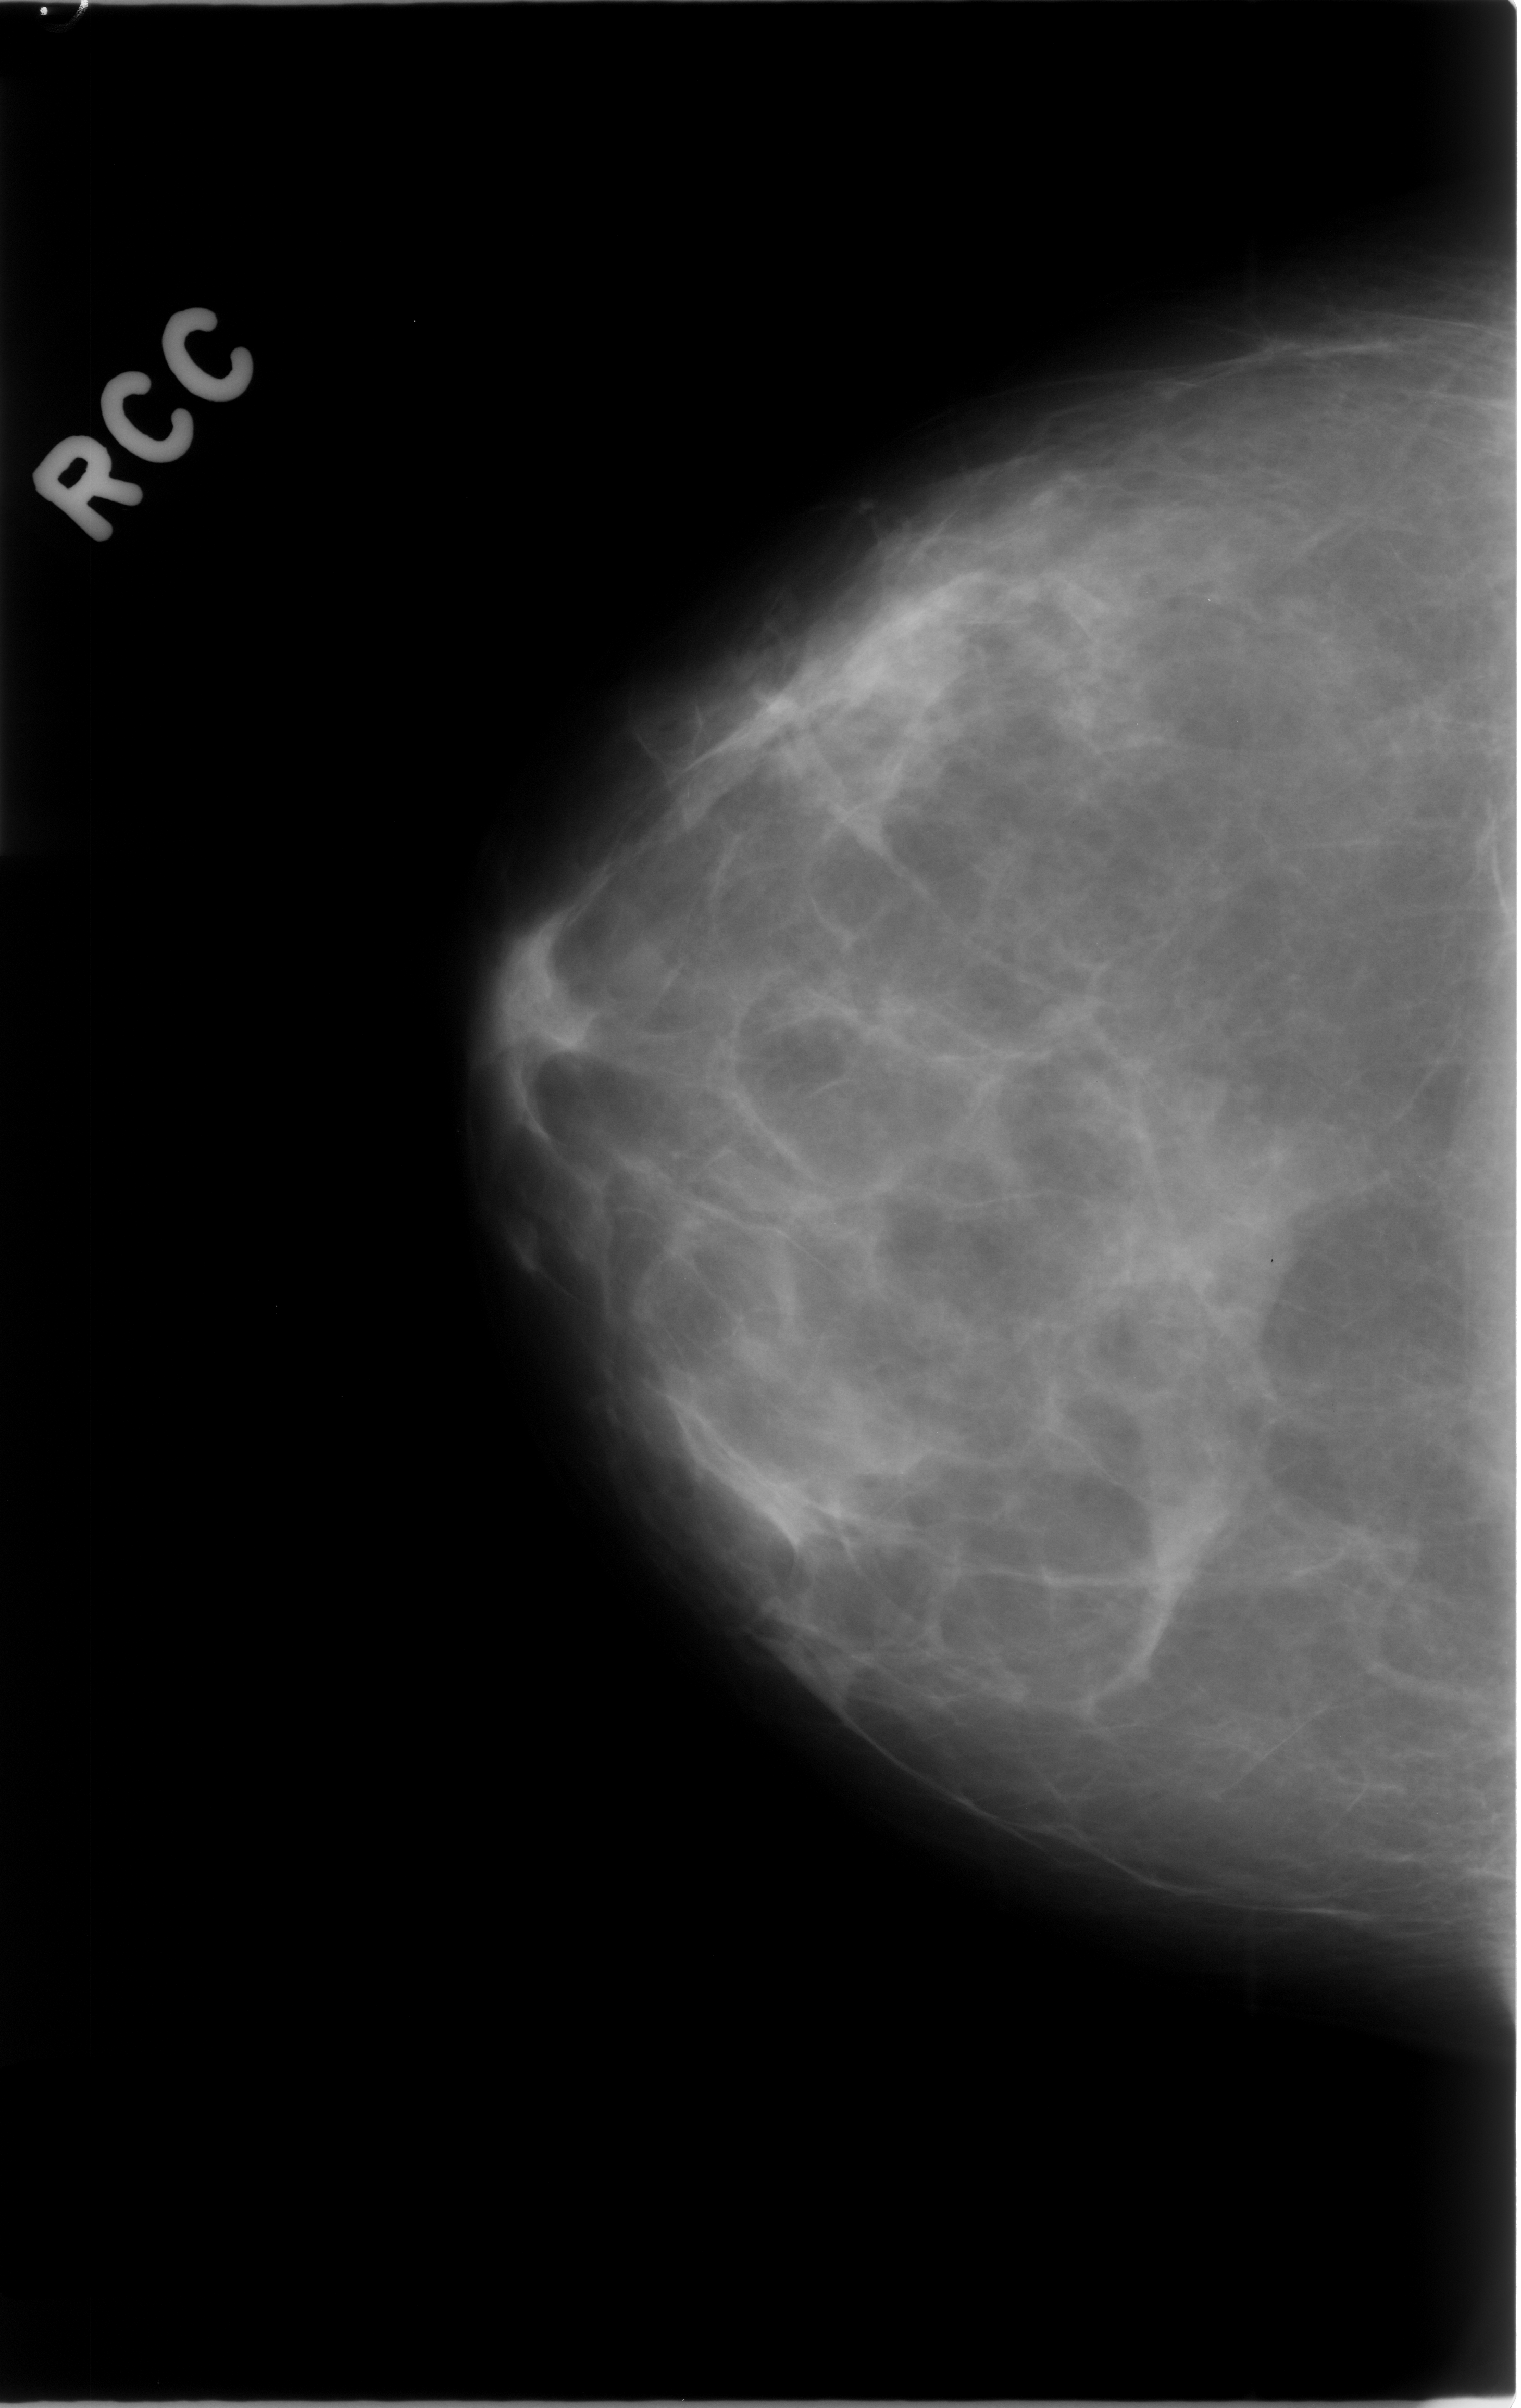
Mammogram (digitized film), right breast, craniocaudal (CC) view, BI-RADS breast density category 2 (scale 1–4).
Abnormality record for this image: mass, shape asymmetric breast tissue, margins ill defined; BI-RADS assessment category 3; subtlety rating 5 on a 1 (subtle) to 5 (obvious) scale; benign without callback (not worked up further).